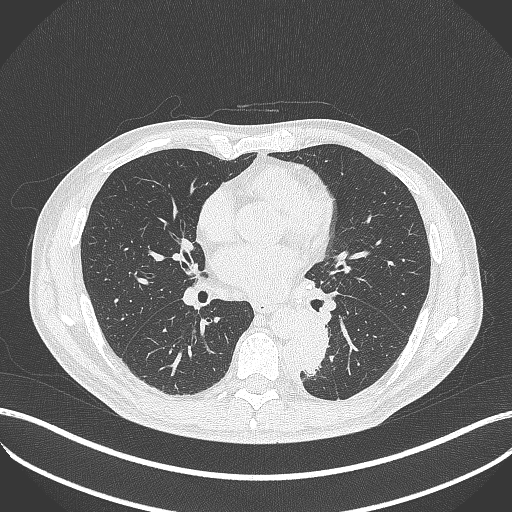
Chest CT, one axial slice; slice 201 of 451 in the series (ordered by position); 120 kVp; lung window (W 1500 / L -600 HU); 512 × 512 image matrix, field of view 400 × 400 mm. Patient: male, 72 years. From the clinical record (not read from this slice): clinical TNM (as recorded): T2b N0 M1.
Annotated regions visible in this slice (rectangle marked by the reading radiologist):
- lung tumour (recorded histology: adenocarcinoma): bounding box [x1, y1, x2, y2] px = [293, 316, 337, 379]